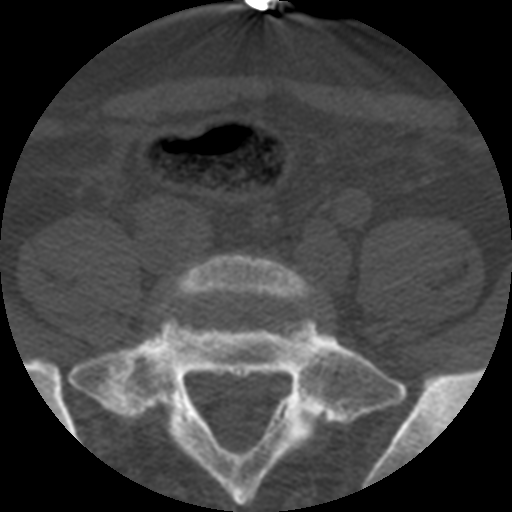
CT including the spine, one axial slice; position 48 of 508 along the scan axis; 120 kVp; bone window (W 1800 / L 400 HU); 1.25 mm slice thickness; 512 × 512 image matrix. Patient age 57 years. From the clinical record (not read from this slice): primary cancer: prostate.
Annotated regions visible in this slice (semi-automatic segmentation, software-assisted and operator-edited):
- L5 vertebra: bounding box (x1, y1, x2, y2) in pixels: (165, 254, 316, 426)